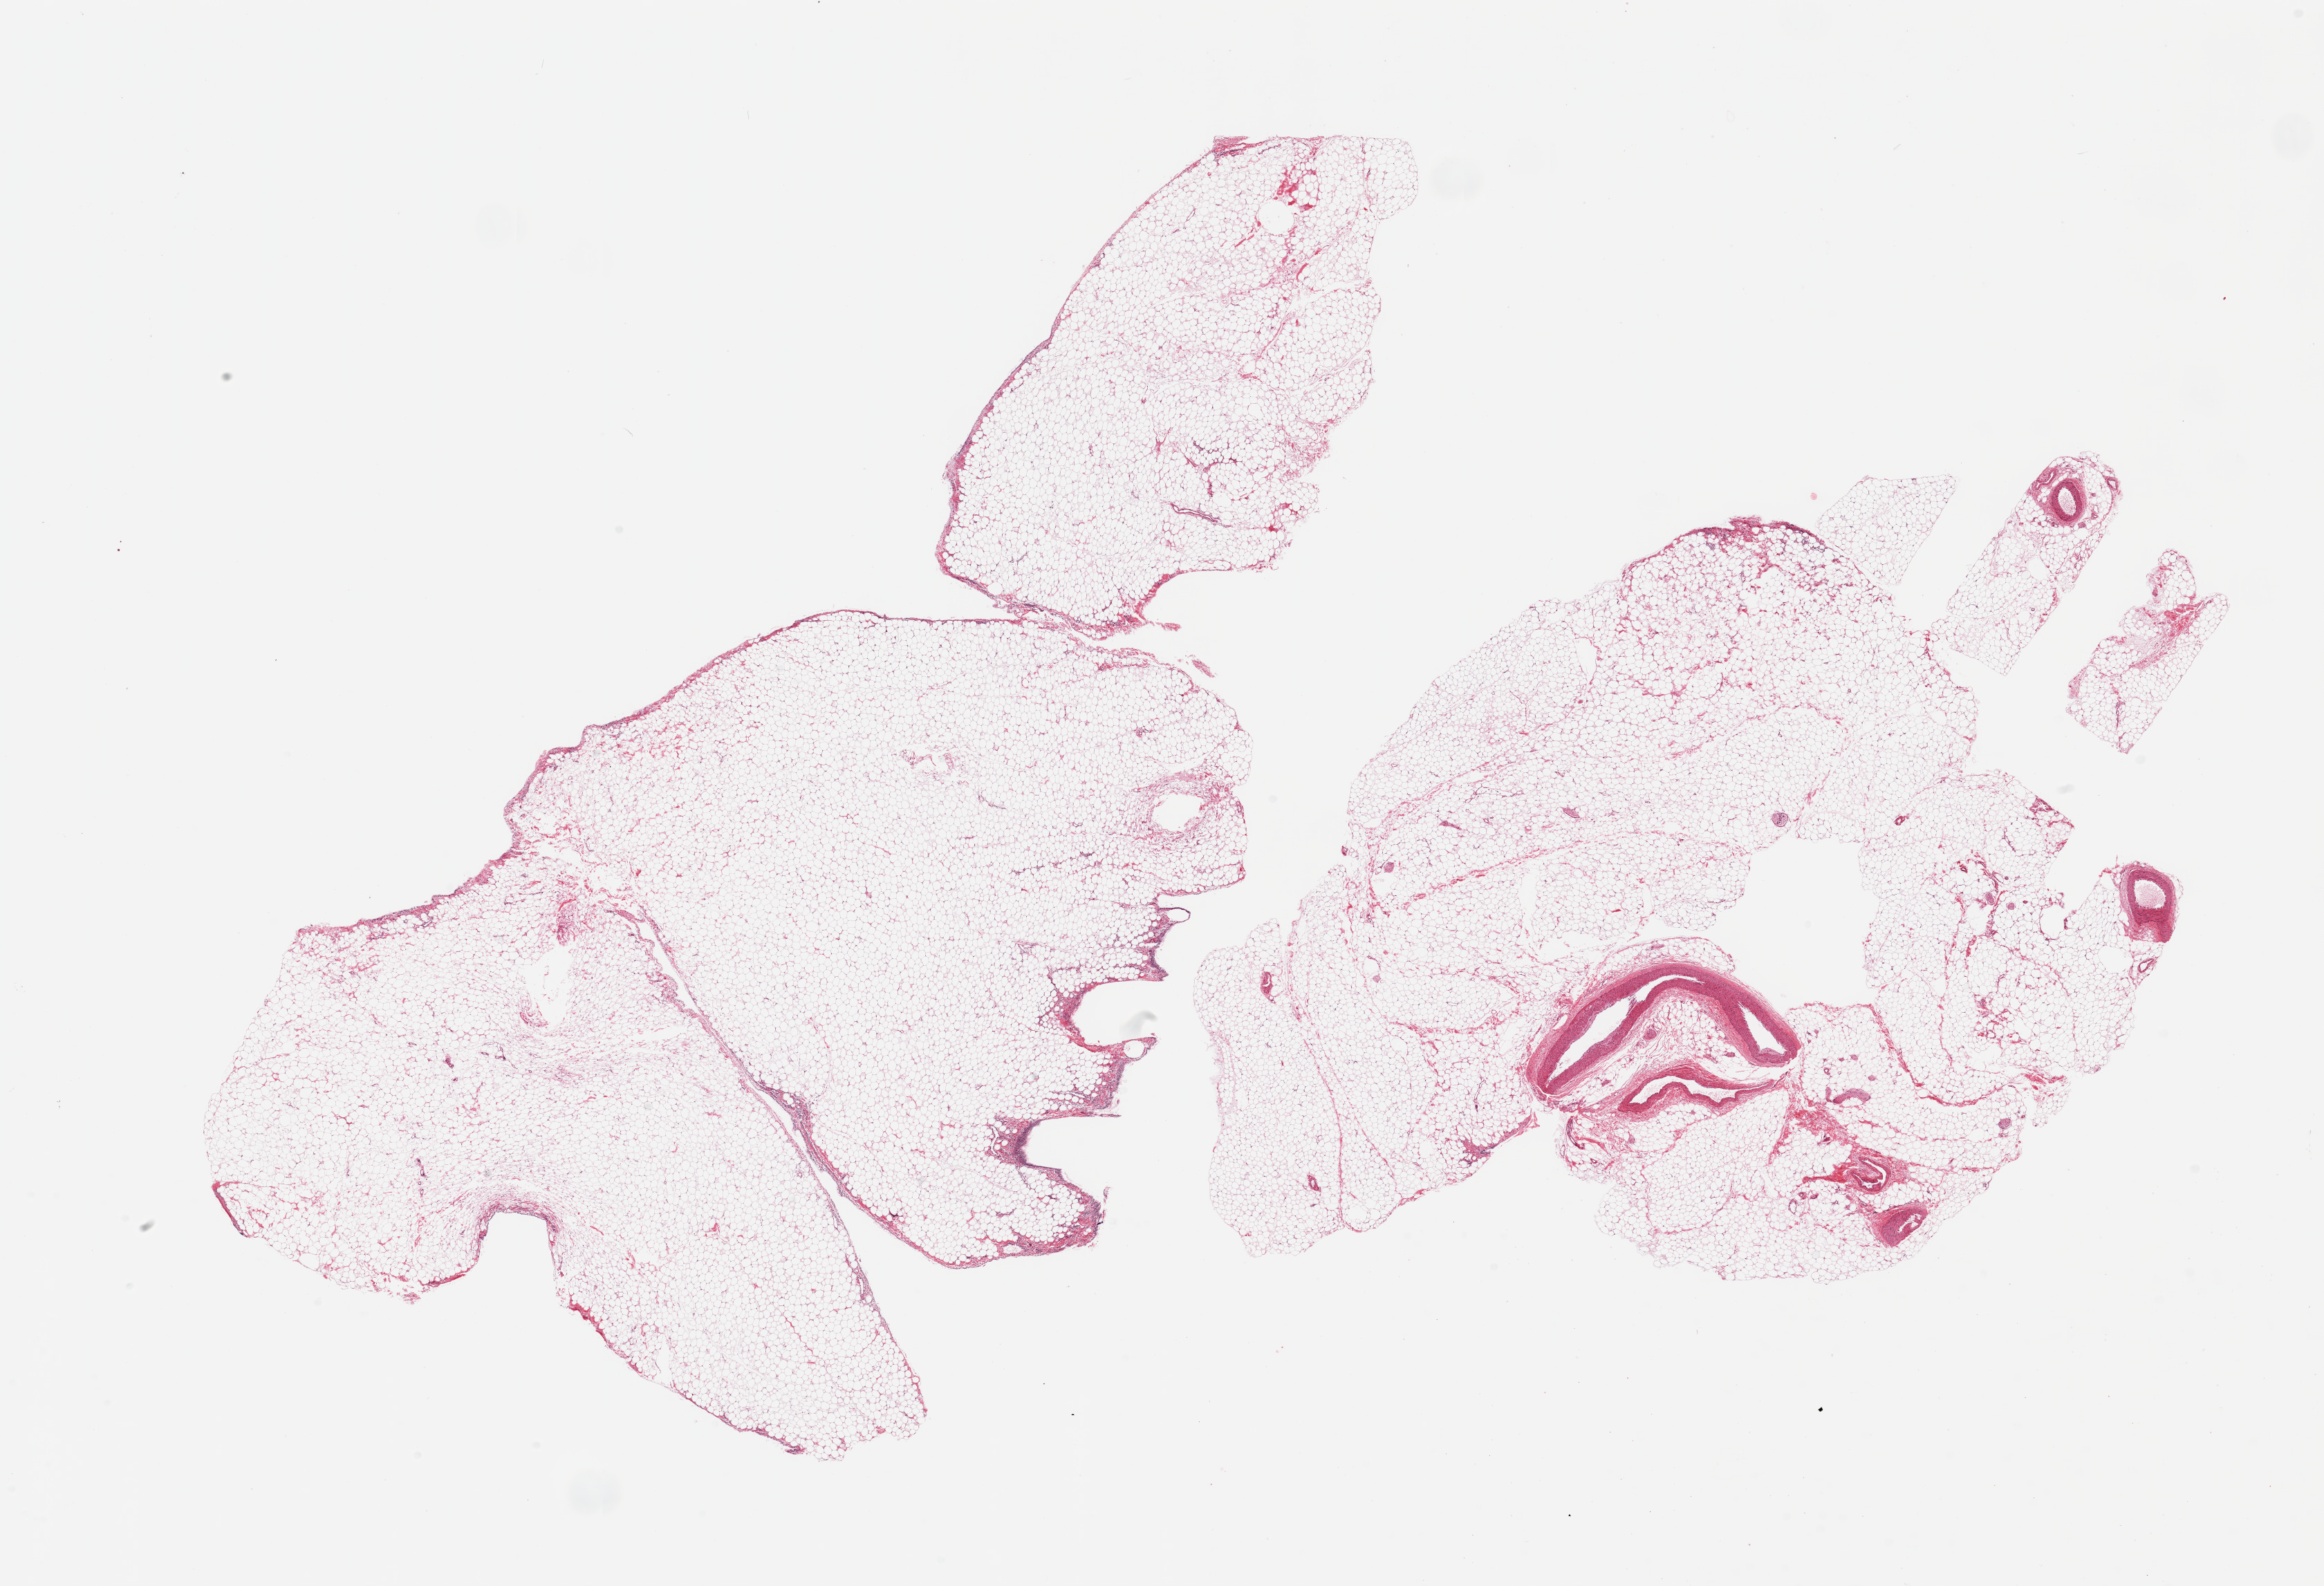
H&E whole-slide image, brightfield, whole scanned area (about 26.6 x 18.1 mm, from a 20x scan) shown as a low-resolution overview, PAXgene-fixed paraffin-embedded (PFPE) section, target tissue: omentum, donor tissue sample. Donor sex: female.
Reviewer comment on this tissue sample: 2 pieces; adipose tissue with few large vessels in 1 piece.